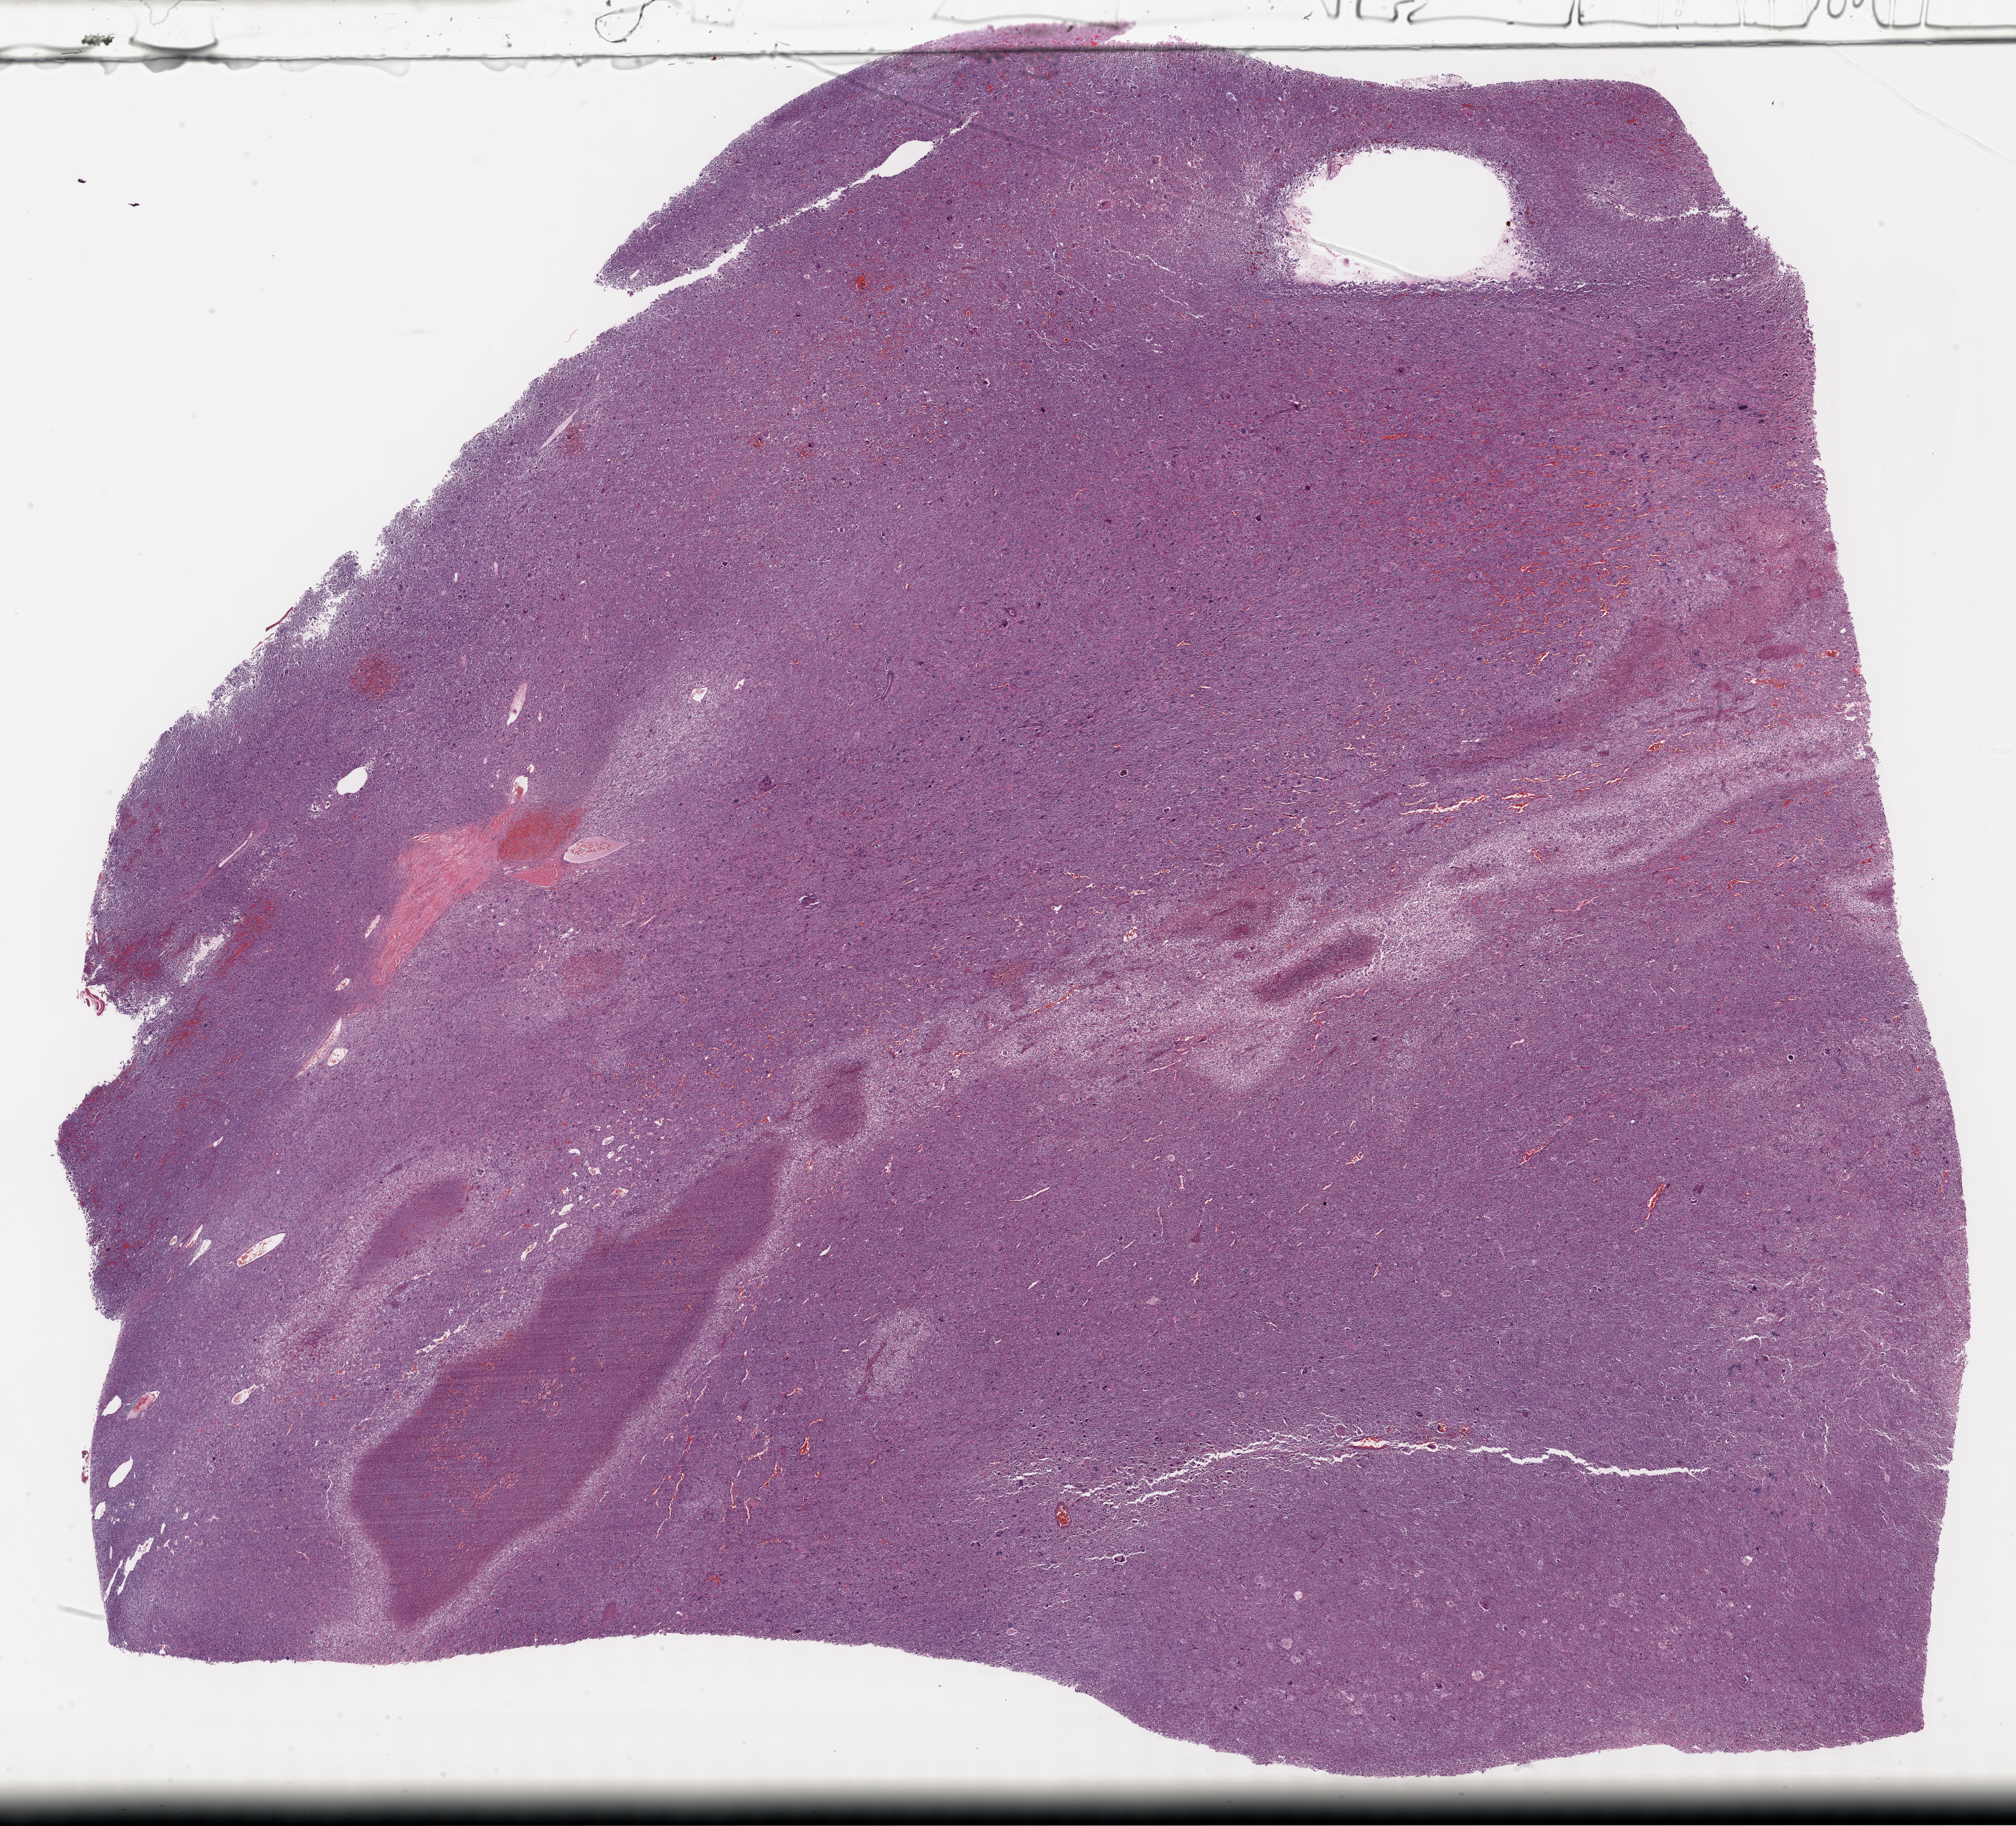
Digitized H&E tissue section (whole slide), low-resolution overview of the scanned area, about 26.2 x 23.7 mm, formalin-fixed paraffin-embedded (FFPE) diagnostic section, connective, subcutaneous and other soft tissues, primary tumour sample. Female, age 68 years at initial diagnosis.
Diagnosis: Undifferentiated sarcoma (connective, subcutaneous and other soft tissues of lower limb and hip).